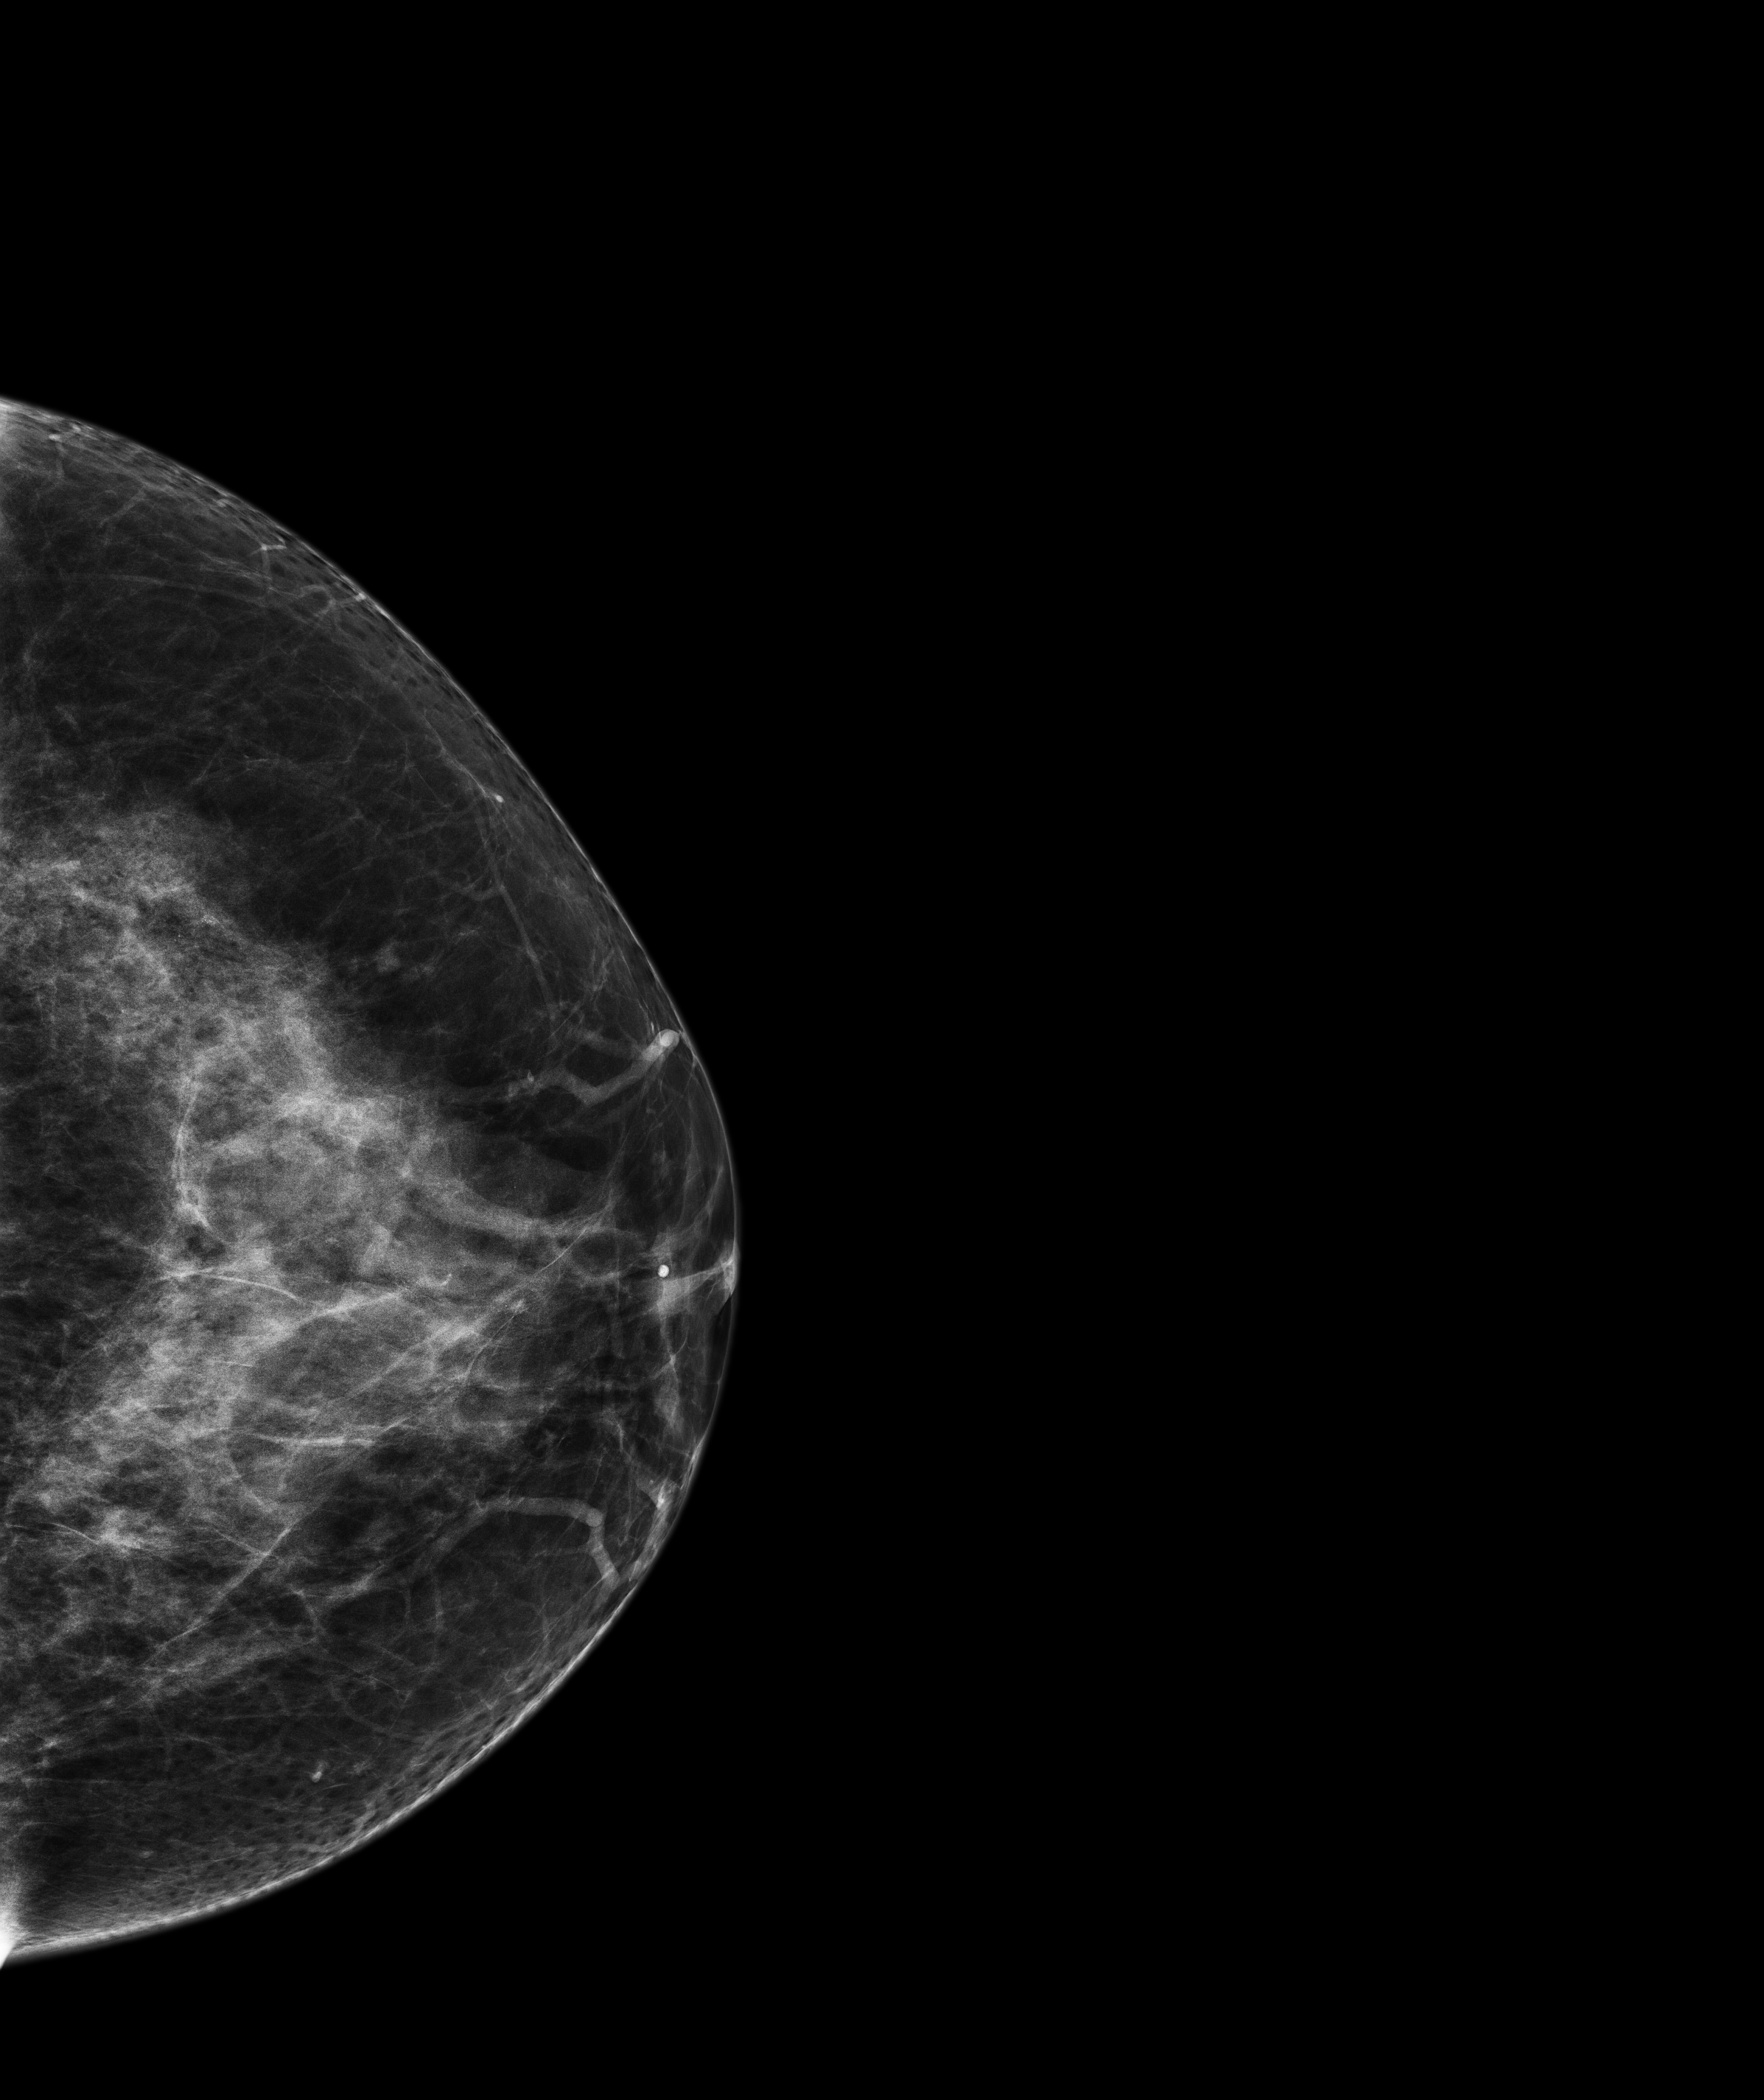
Screening examination; compressed breast thickness 70 mm. Patient: female, 48 years.
Image type: full-field digital mammogram. Breast: left. Projection: cranio-caudal projection.